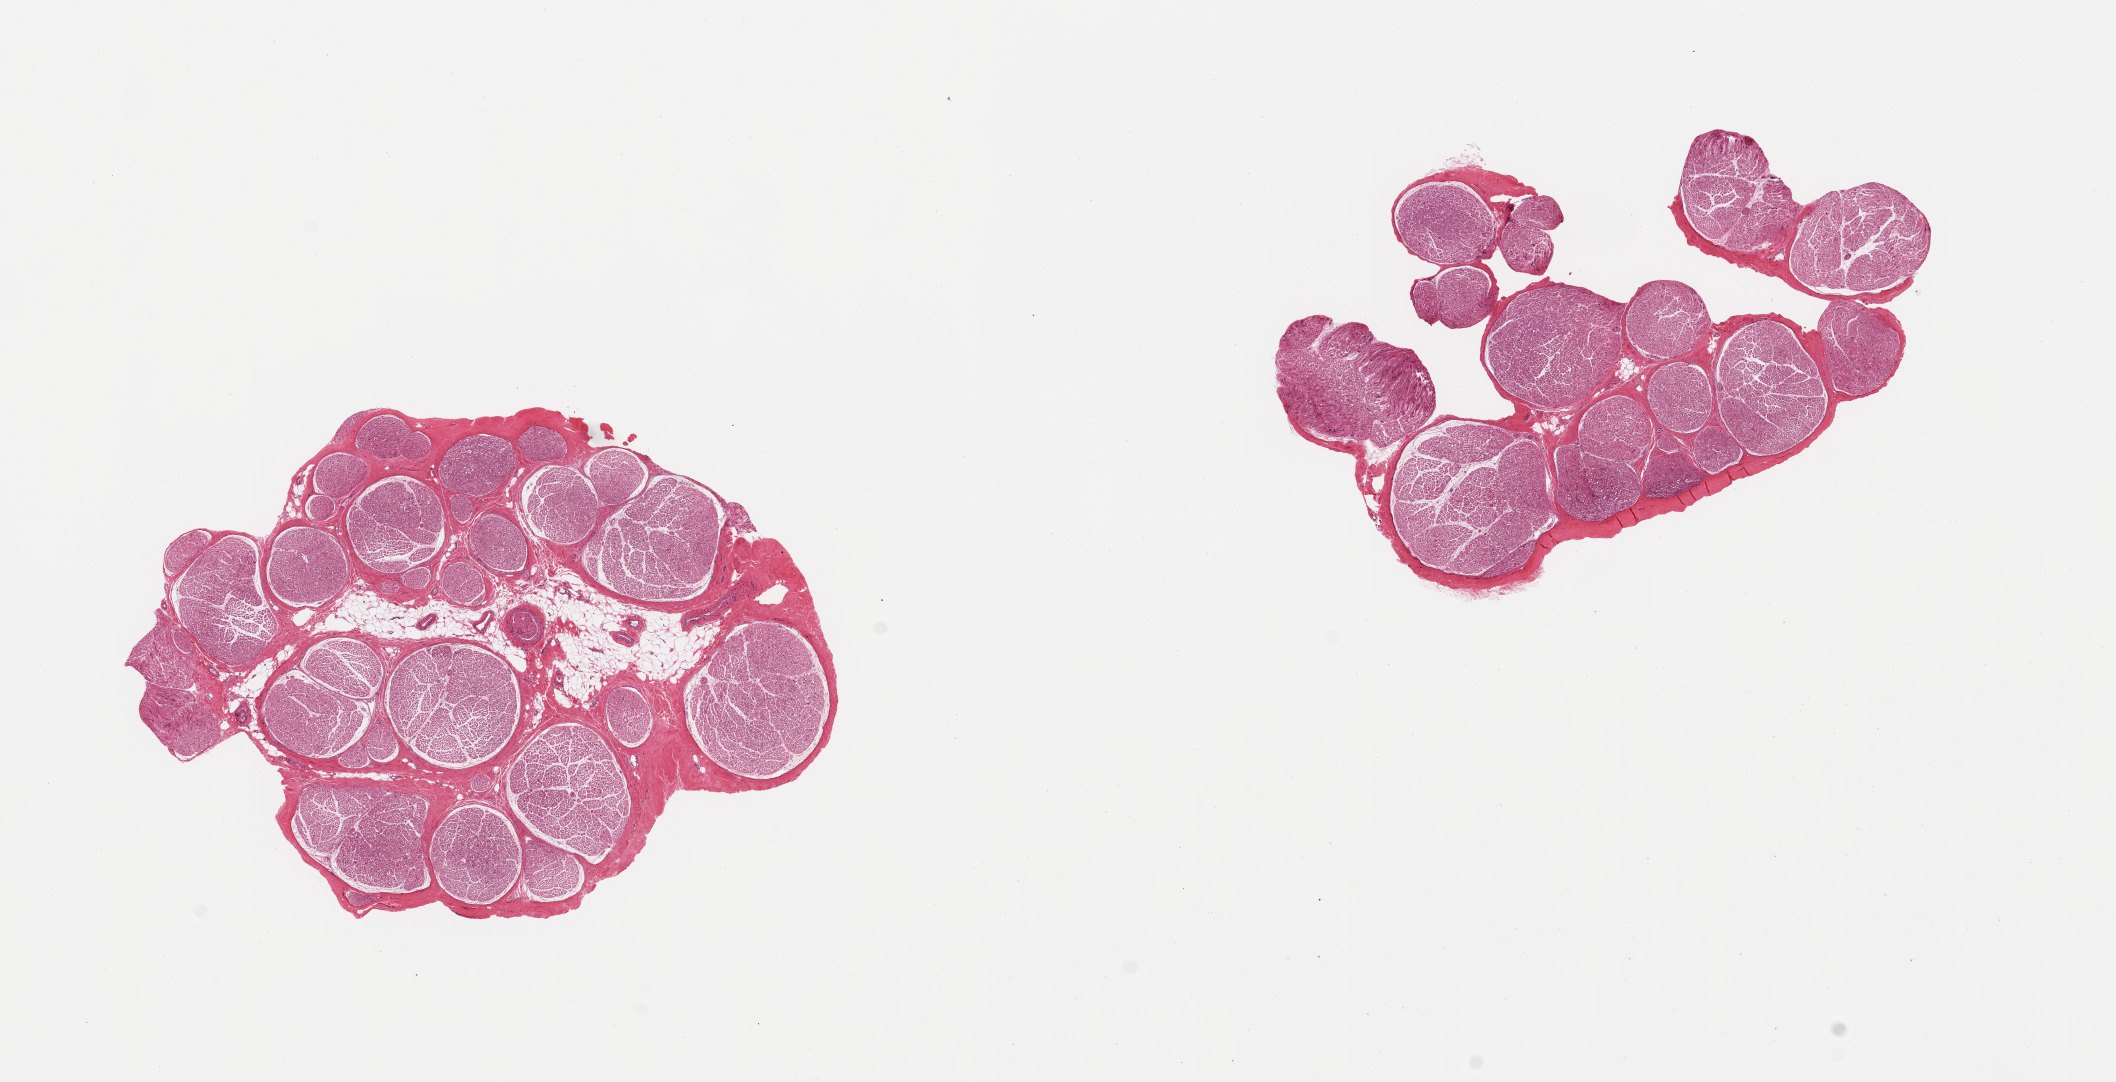
Digitized hematoxylin and eosin (H&E)-stained section, a low-resolution overview of the entire scanned area, about 16.7 x 8.6 mm, PAXgene-fixed paraffin-embedded (PFPE) section, section of tibial nerve (target tissue), donor tissue sample. Male donor.
Review note (as recorded): 2 pieces; well trimmed; 20% internal fat in one.